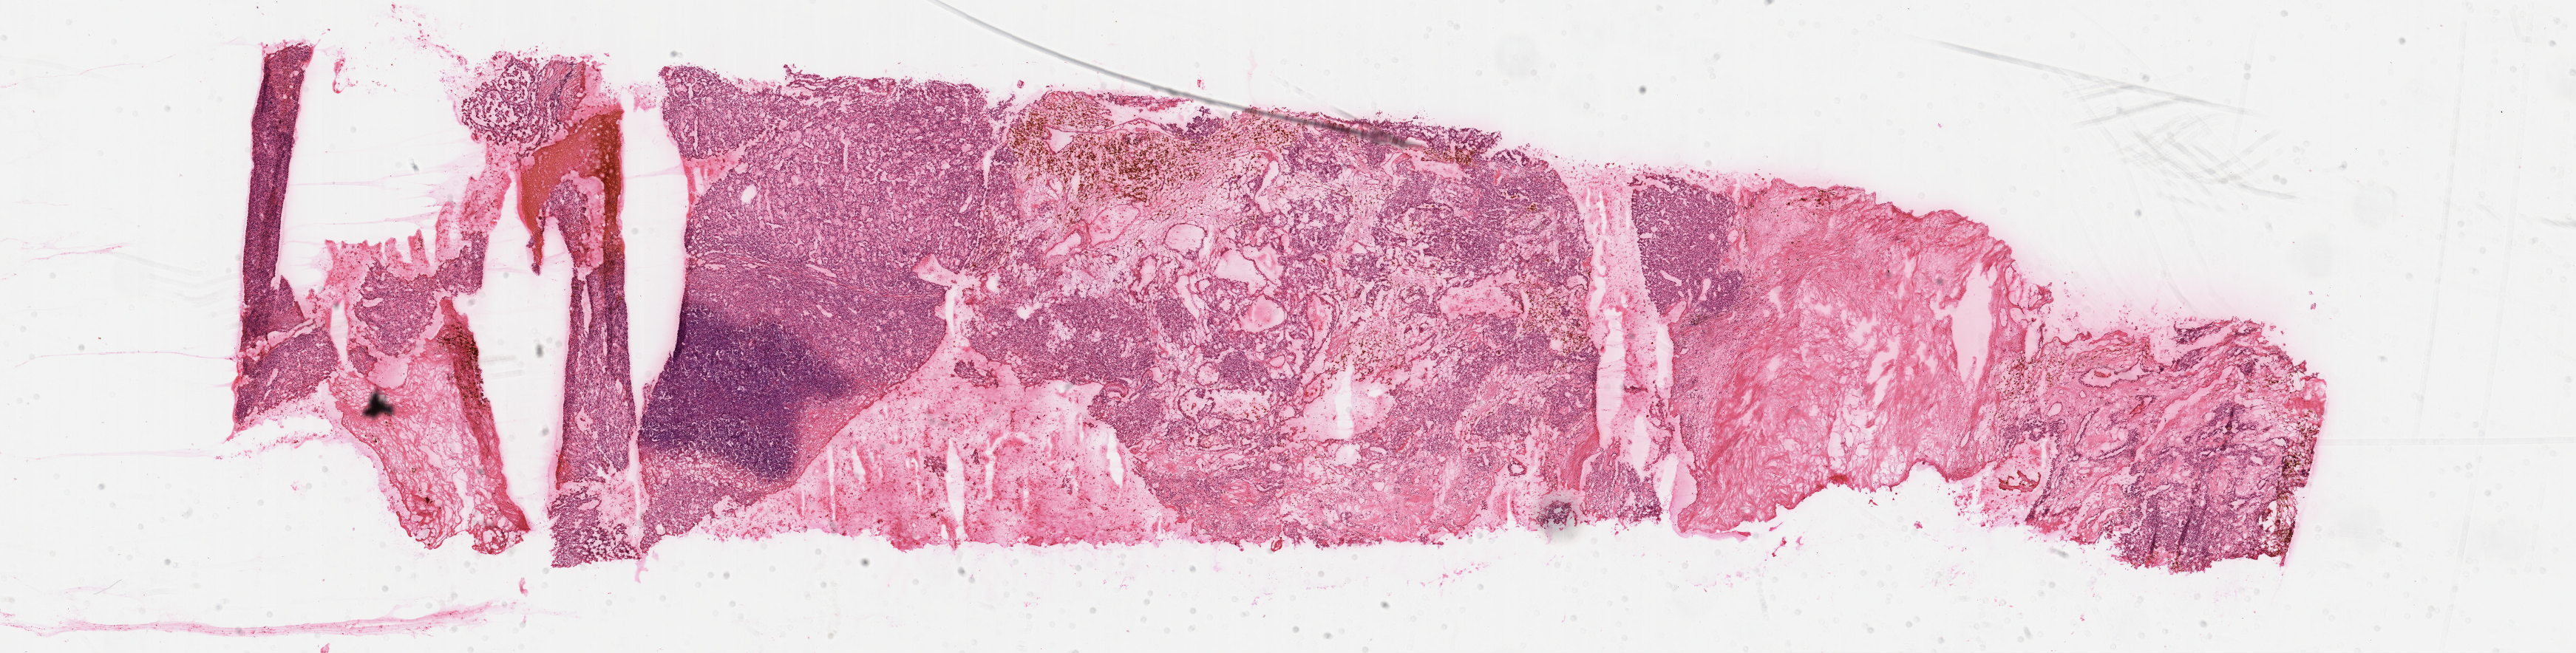
H&E whole-slide image, whole scanned area (about 28.2 x 7.2 mm) shown as a low-resolution overview. Formalin-fixed paraffin-embedded (FFPE) diagnostic section. Sample: primary tumour, kidney. Patient sex: male. Histologic grade: G4 (undifferentiated).
AJCC pathologic stage: I. Histologic diagnosis: Clear cell adenocarcinoma, NOS.